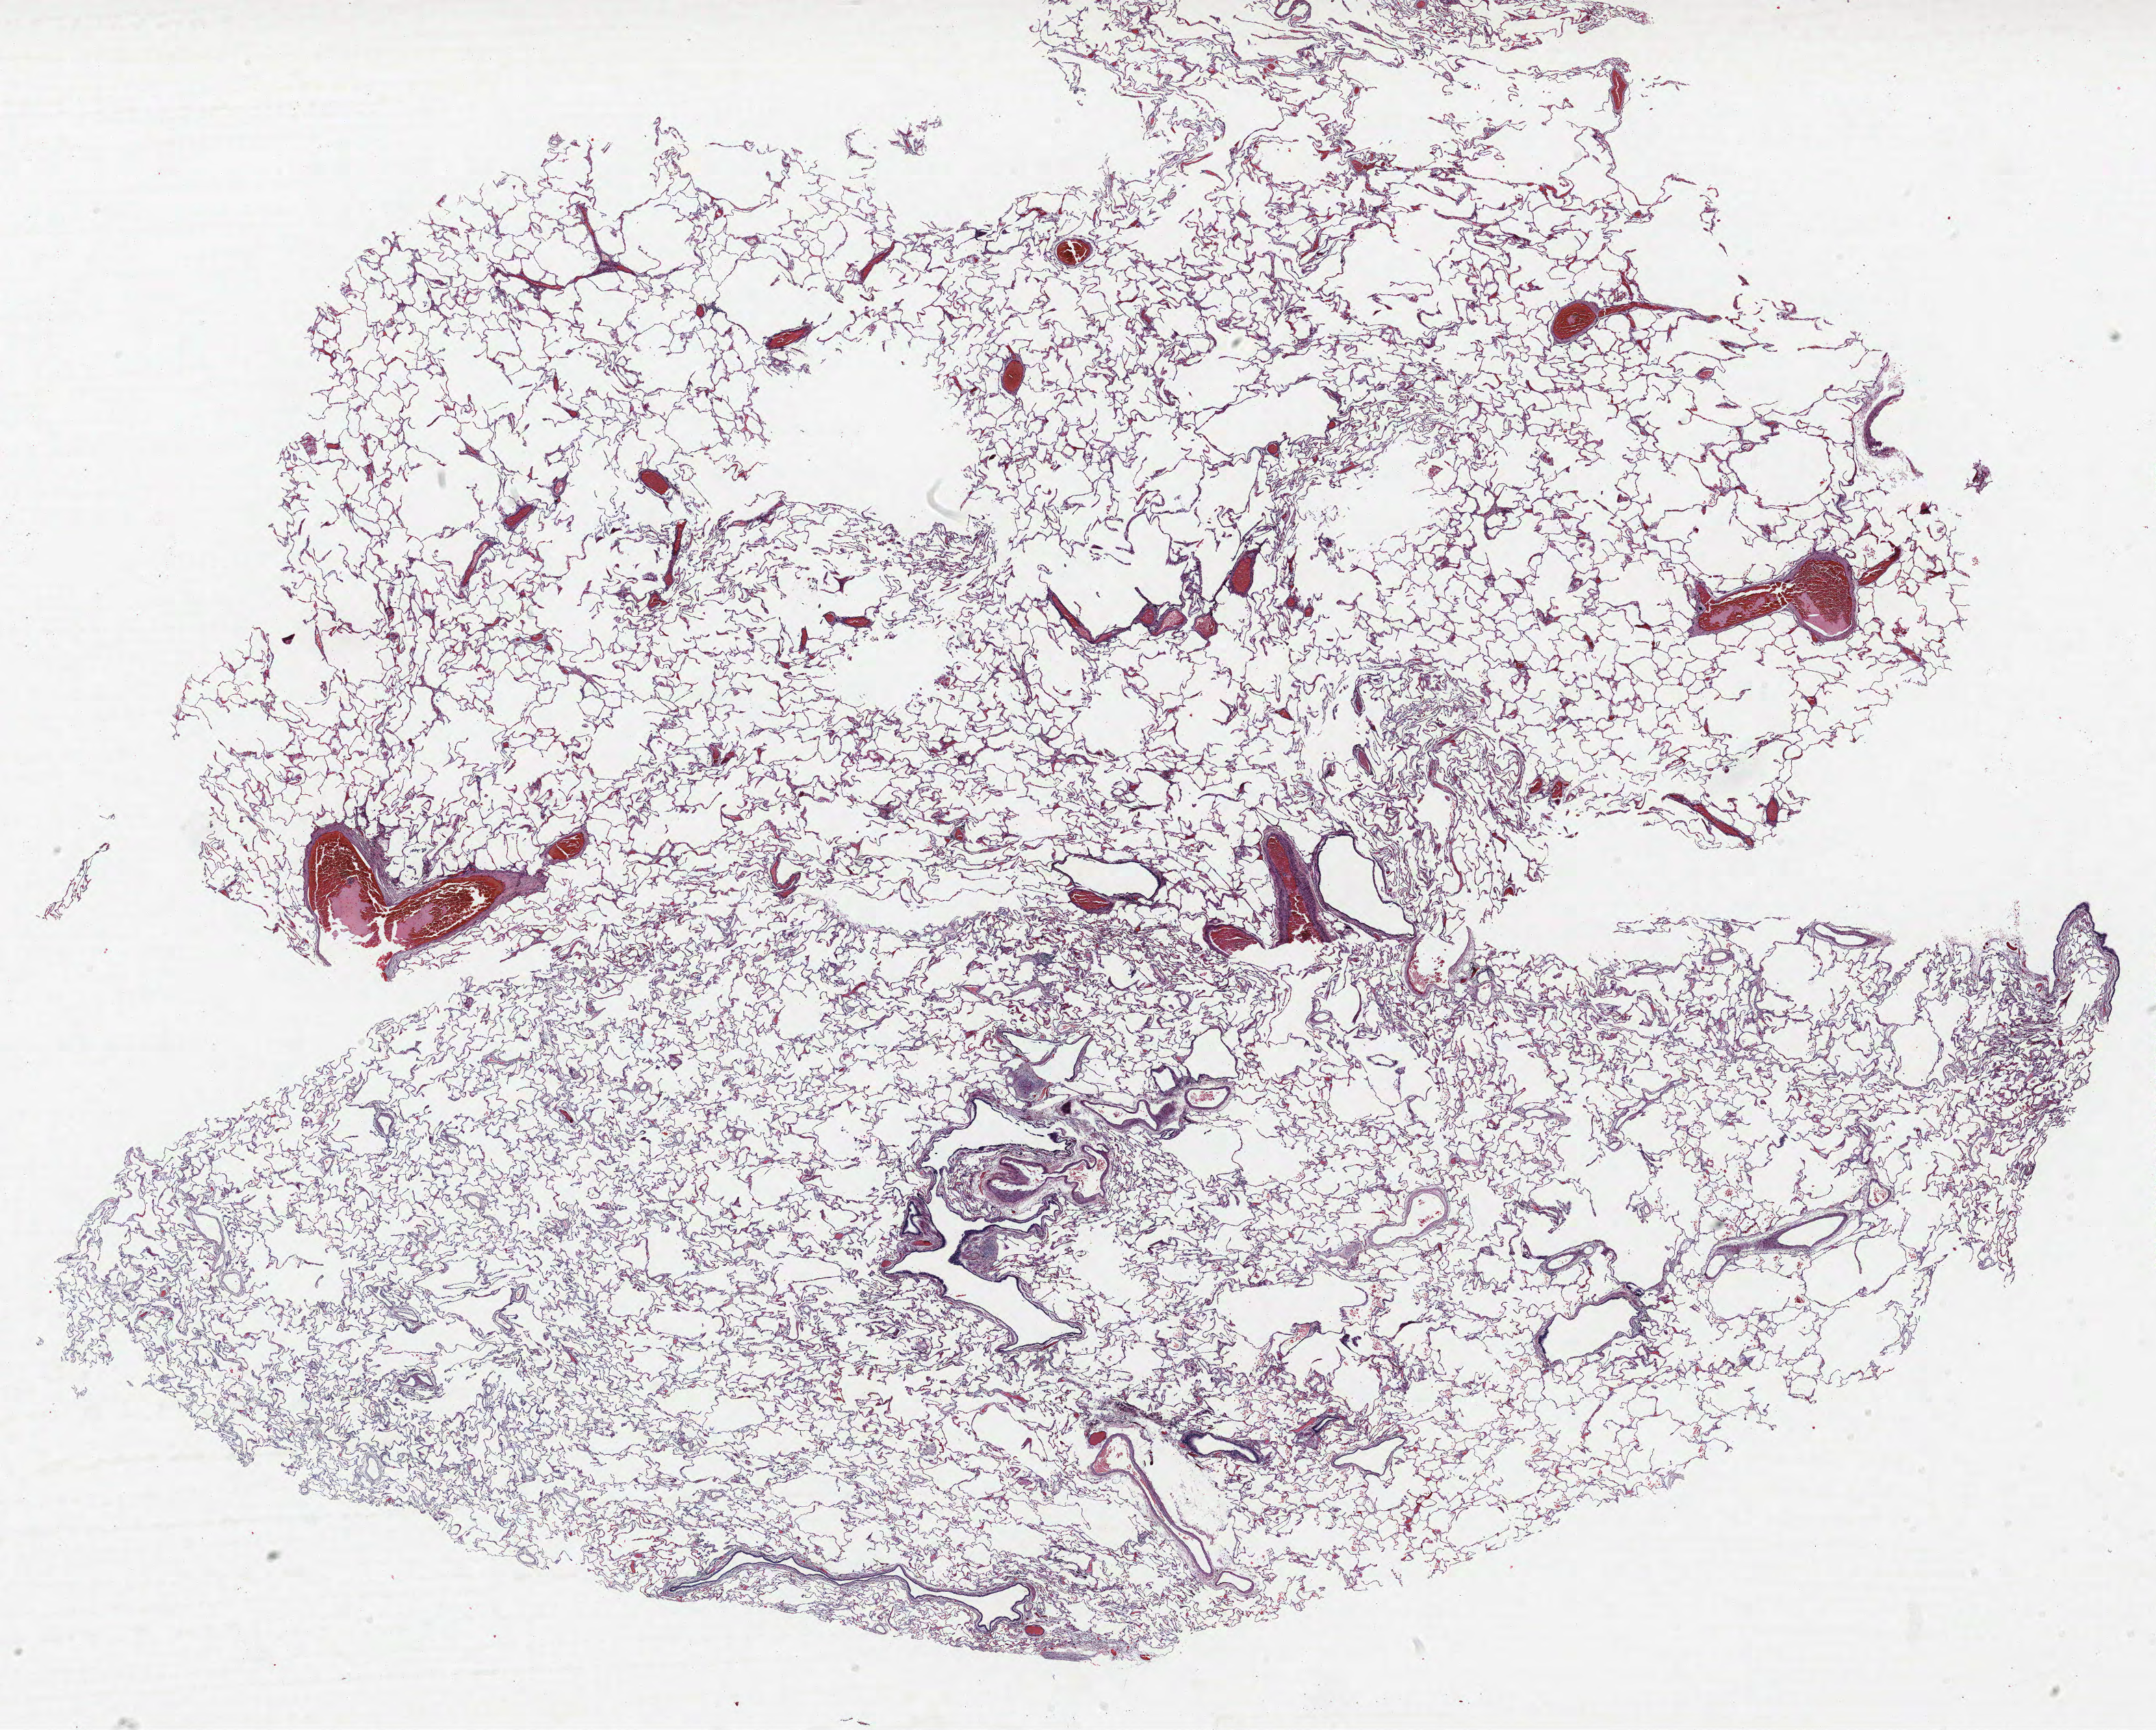
Hematoxylin and eosin (H&E) stained whole-slide image — low-resolution overview of the scanned area, about 25.2 x 20.2 mm, FFPE section, lung. Female patient, aged 65 at enrolment. Grade: moderately differentiated (G2).
• tumour size (pathology): 90 mm
• stage (AJCC 6th edition): IIB
• primary tumour location (clinical record): left lower lobe
• ICD-O-3 topography: lower lobe of lung (C34.3)
• participant's lung-cancer diagnosis: Squamous cell carcinoma, NOS